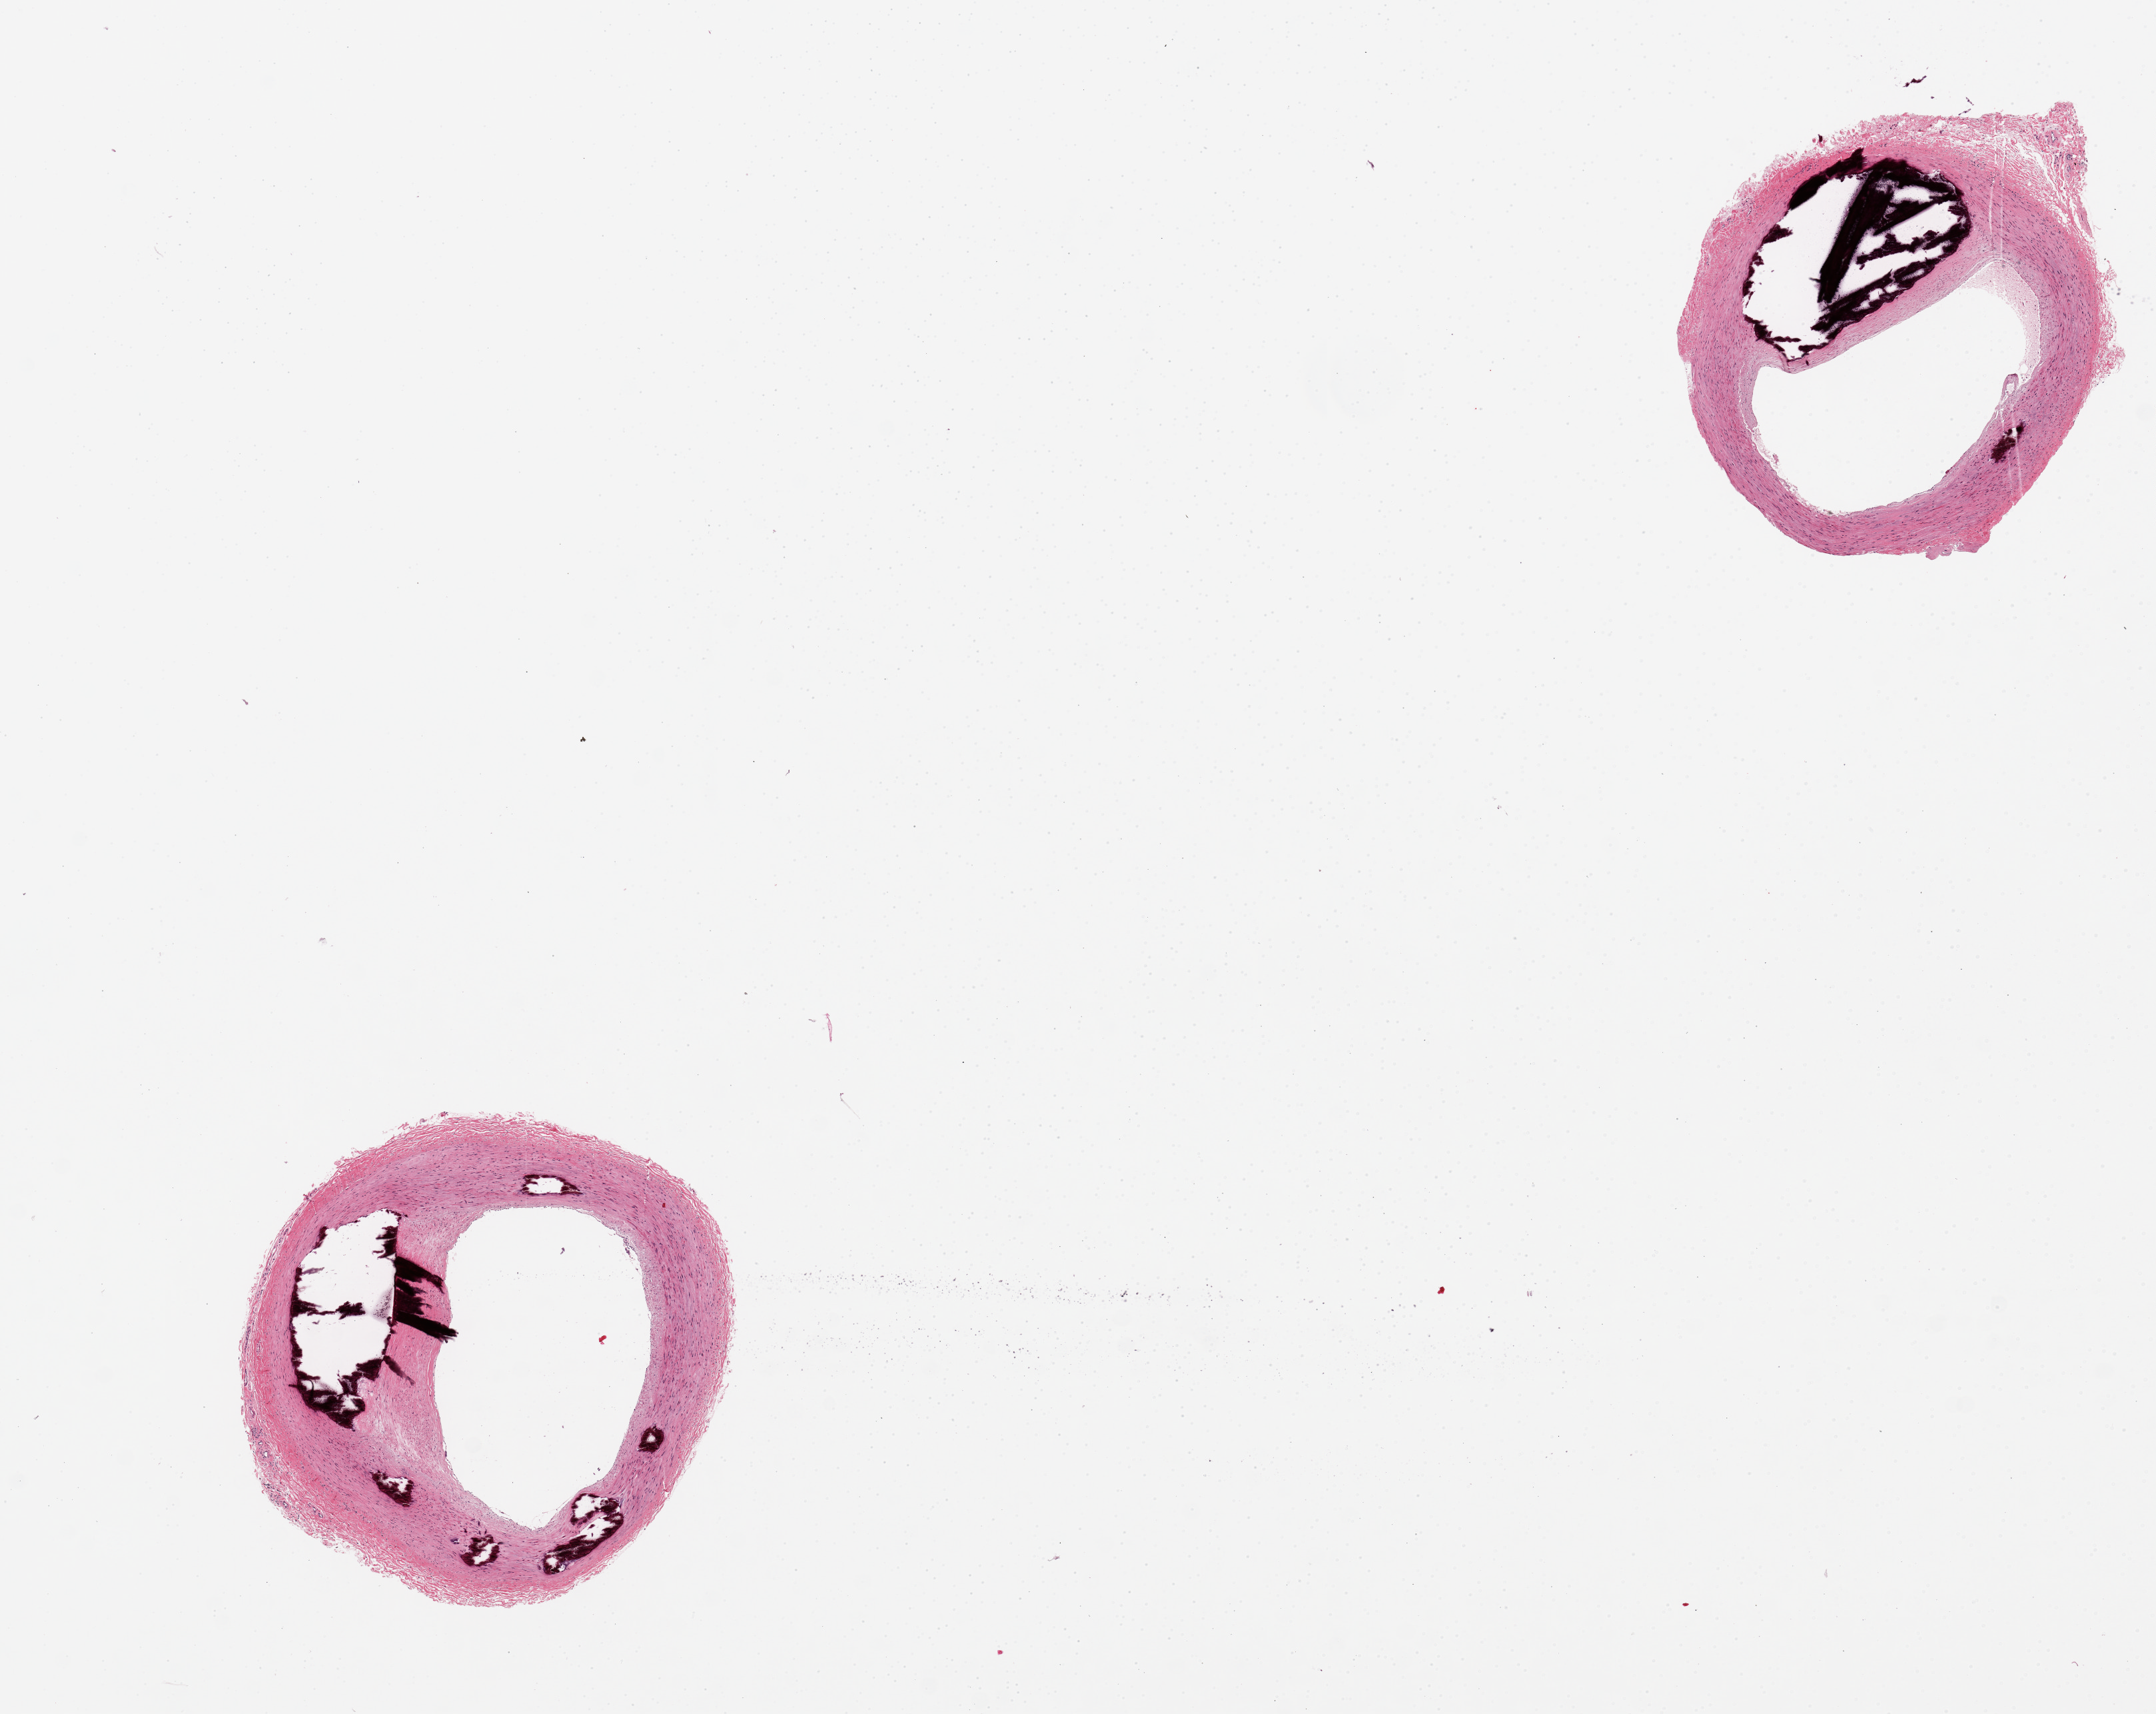
Digitized hematoxylin and eosin (H&E)-stained section — shown as a low-resolution overview of the whole scanned area (about 12.8 x 10.2 mm, acquisition: 20x scan), PAXgene-fixed, paraffin-embedded tissue, sampled site (target tissue): tibial artery, tissue donor sample. Male donor.
Pathologist's review note for this sample: 2 pieces. 30-40% occlusion by calcified plaques.